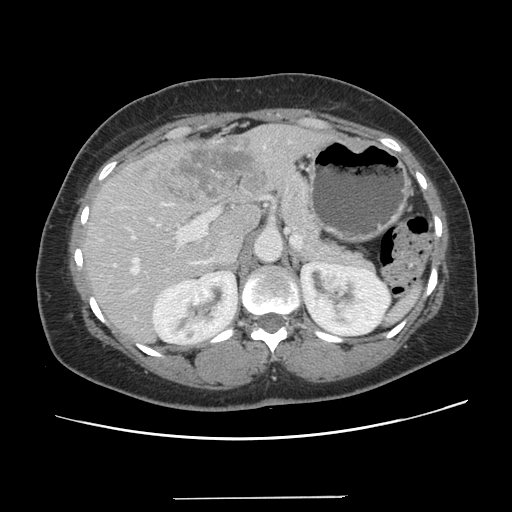
Contrast-enhanced abdominal CT, one axial slice; slice 79 of 141 in the series (ordered by position); intravenous contrast given; soft-tissue window (W 400 / L 40 HU); 2.5 mm slice thickness; 512 × 512 image matrix, field of view 366 × 366 mm. Female patient, age 53 years. From the clinical record (not read from this slice): diagnosis: colorectal cancer liver metastases, imaged before liver resection; multiple liver metastases: no; largest metastasis: 14.5 cm; disease in both lobes: yes.
Structures marked on this image (outlined manually by an expert reader):
- hepatic veins: bounding box [x1, y1, x2, y2] px = [130, 258, 138, 273]
- liver: [84, 125, 330, 343]
- planned liver remnant (the part of the liver to remain after resection): [85, 205, 261, 343]
- portal vein (with intrahepatic branches): [132, 203, 217, 272]
- liver metastasis: [139, 136, 266, 204]